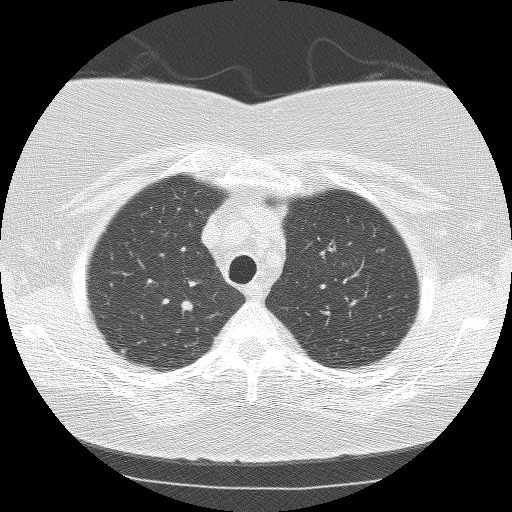
Axial slice from a low-dose chest CT screening exam. Baseline screening round. Lung window (W 1500 / L -600 HU). 2.5 mm slice thickness. Lung (sharp) reconstruction kernel (BONE). 120 kVp. Slice 26 of 159 in the series. Female, age 64 years at enrolment. Current smoker at enrolment.
Expert-annotated lung lesion, bounding box [x1, y1, x2, y2] px = [168, 291, 210, 328]. The exam's reader record, not a measurement of the box and not confirmed to be the same lesion: non-calcified nodule or mass ≥4 mm, right upper lobe, 7 × 7 mm, smooth margins, soft tissue attenuation. Official screen result: positive, change unspecified: nodule(s) >= 4 mm or enlarging nodule(s), mass(es), or other non-specific abnormalities suspicious for lung cancer. Participant outcome: lung cancer diagnosed 314 days after this screen — small cell carcinoma, NOS, right hilum, stage IV (AJCC 6th edition).